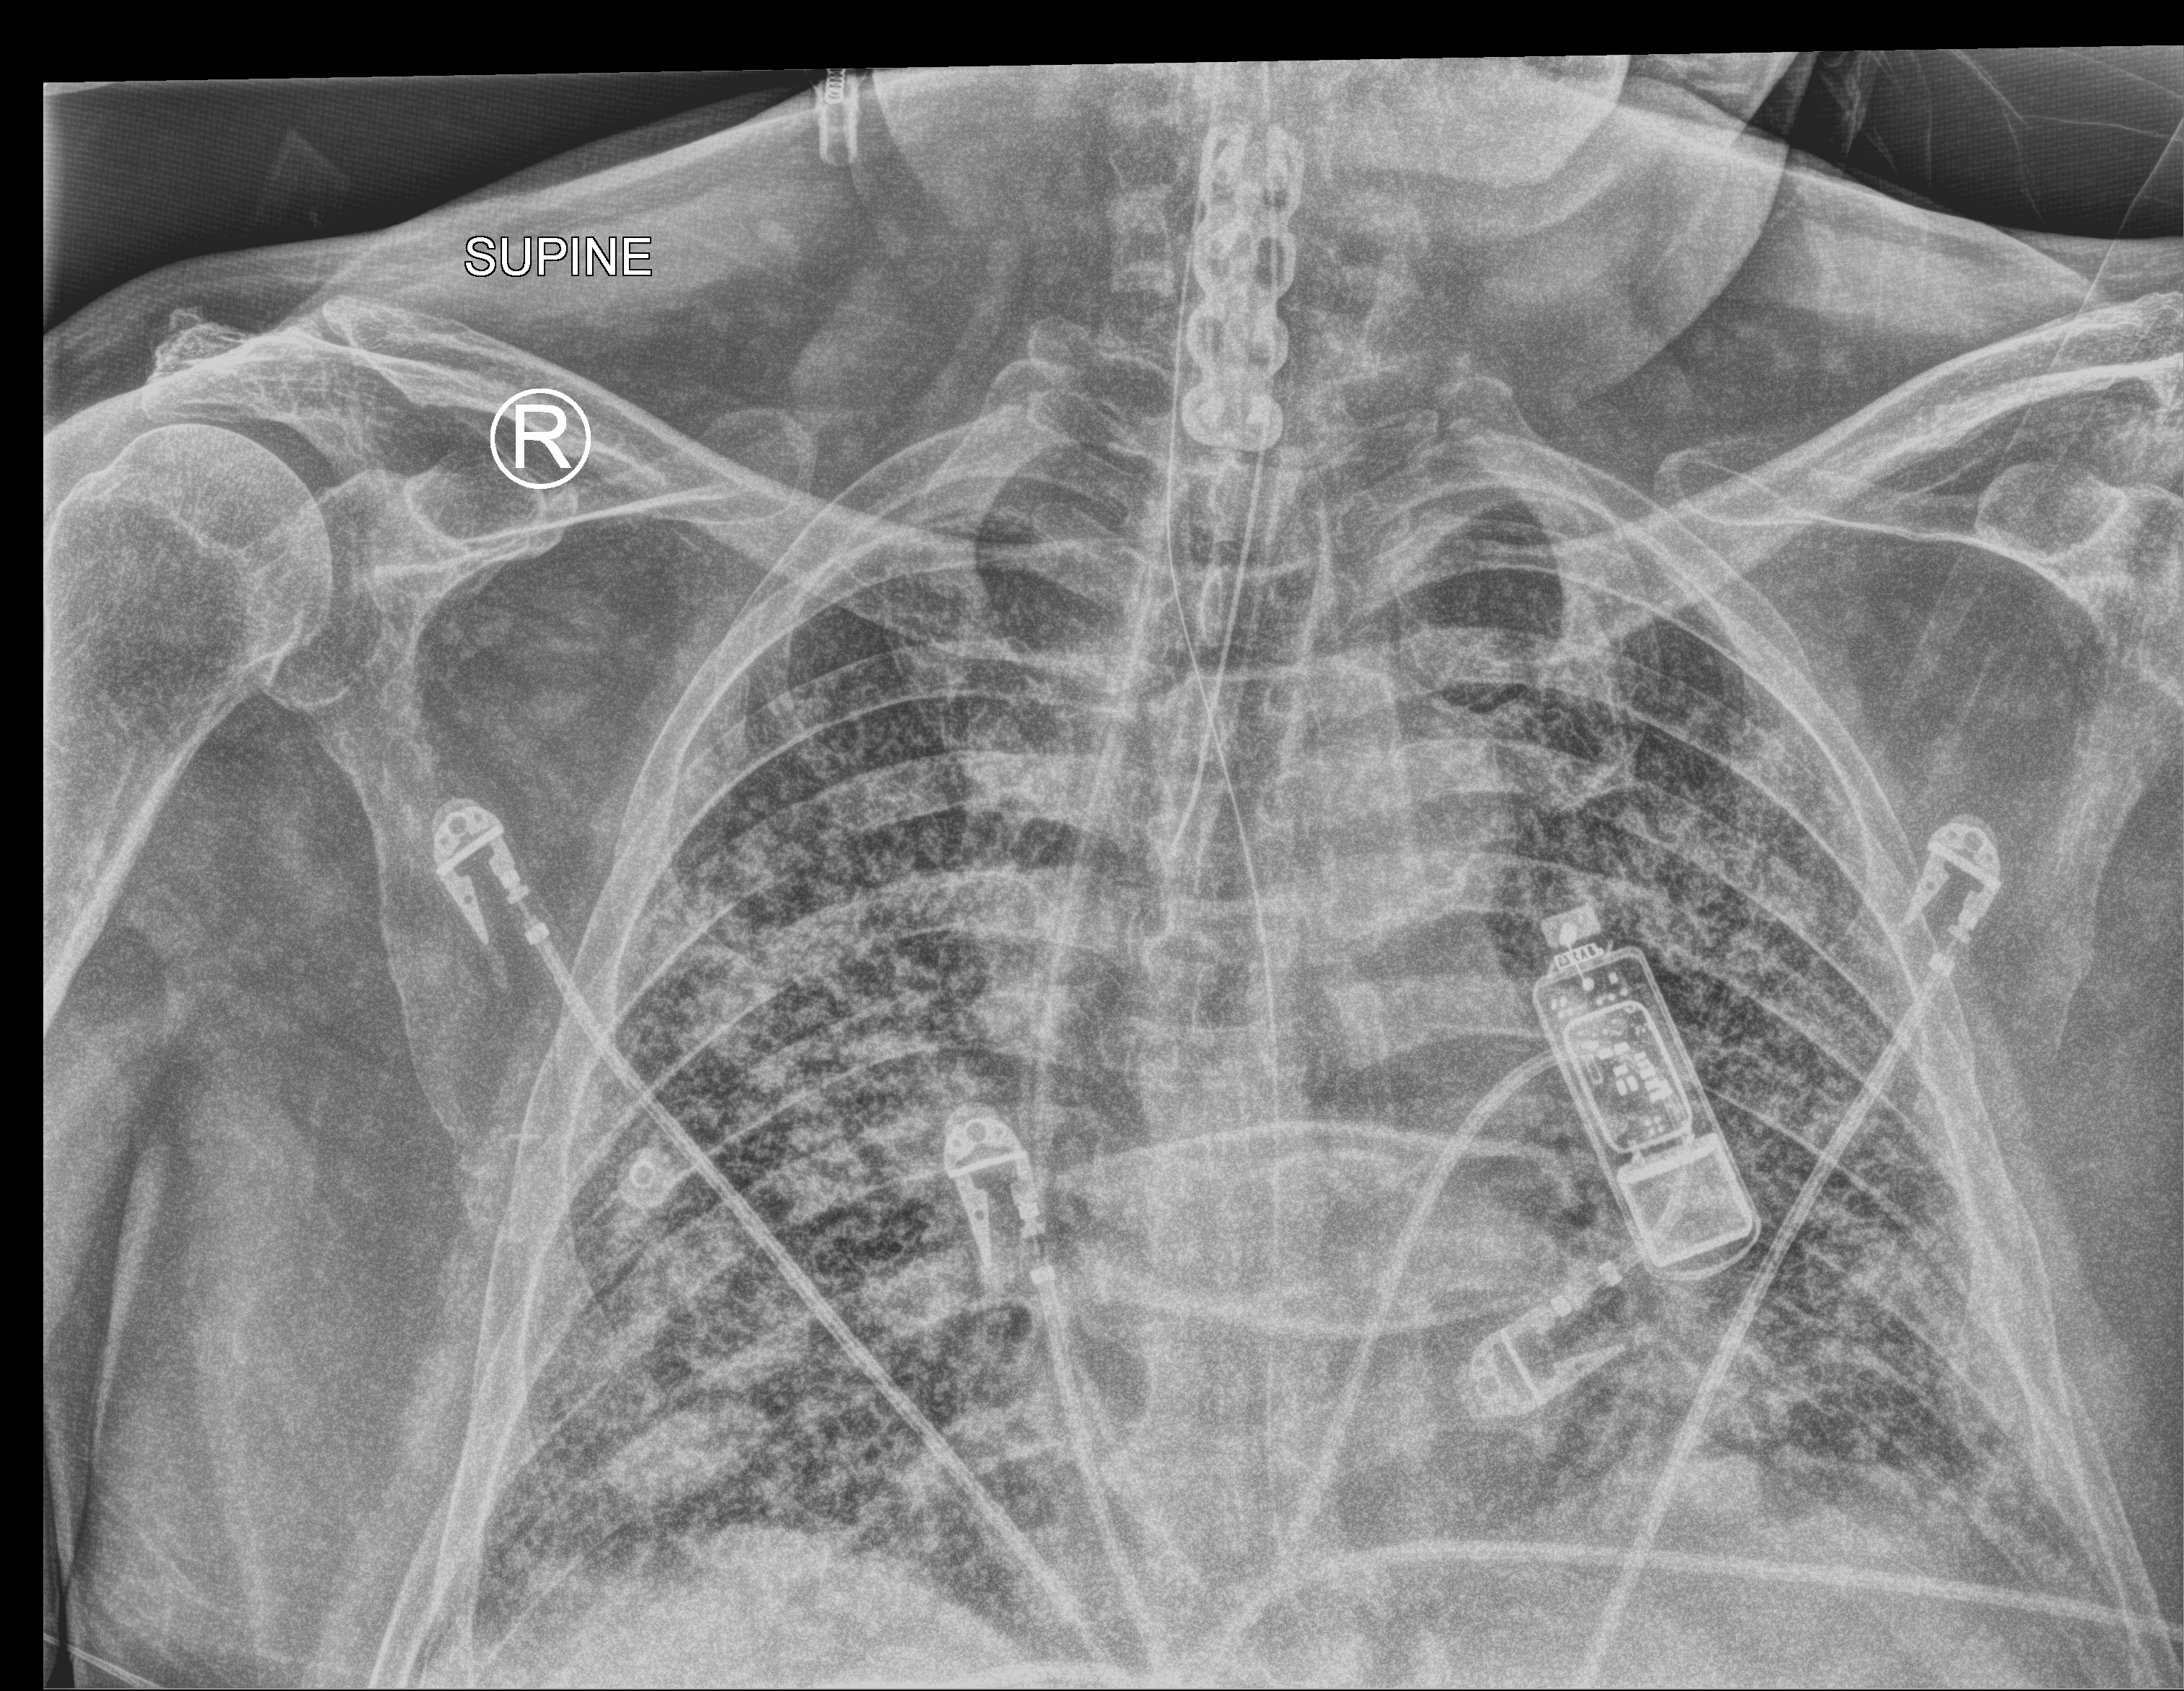
Chest X-ray (portable), anteroposterior (AP) projection. Patient hospitalised with COVID-19; male, aged 60–74 years.
From the hospital-stay record, not from the radiograph (when in the stay this image was taken is not recorded): other chronic lung disease (admission record): yes.